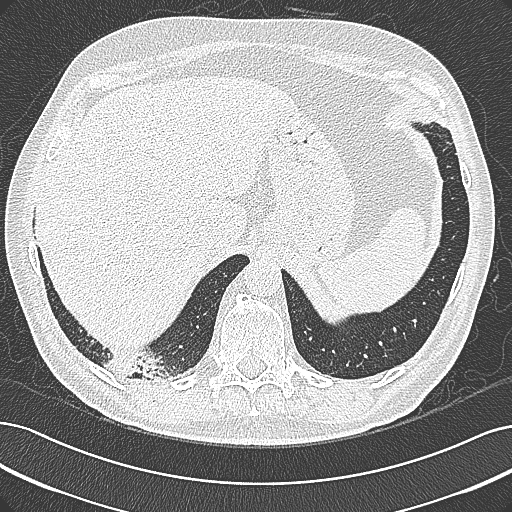
Axial slice from a low-dose chest CT screening exam. Baseline annual screen. Lung window (W 1500 / L -600 HU). 1 mm slice thickness. Lung (sharp) reconstruction kernel (B80f). Slice 258 of 355 in the series. 512 × 512 image matrix, field of view 362 × 362 mm. Male, age 68 years at enrolment.
• Lesion marked by an expert reader, bounding box [x1, y1, x2, y2] px = [94, 336, 195, 396].
• No non-calcified nodule or mass ≥4 mm was recorded by the screening reader at this exam.
• Official screen result: negative screen, significant abnormalities not suspicious for lung cancer.
• Later outcome: lung cancer diagnosed 154 days after this screen — mucinous adenocarcinoma, right lower lobe, well differentiated (G1), stage IB (AJCC 6th edition), 50 mm at pathology.